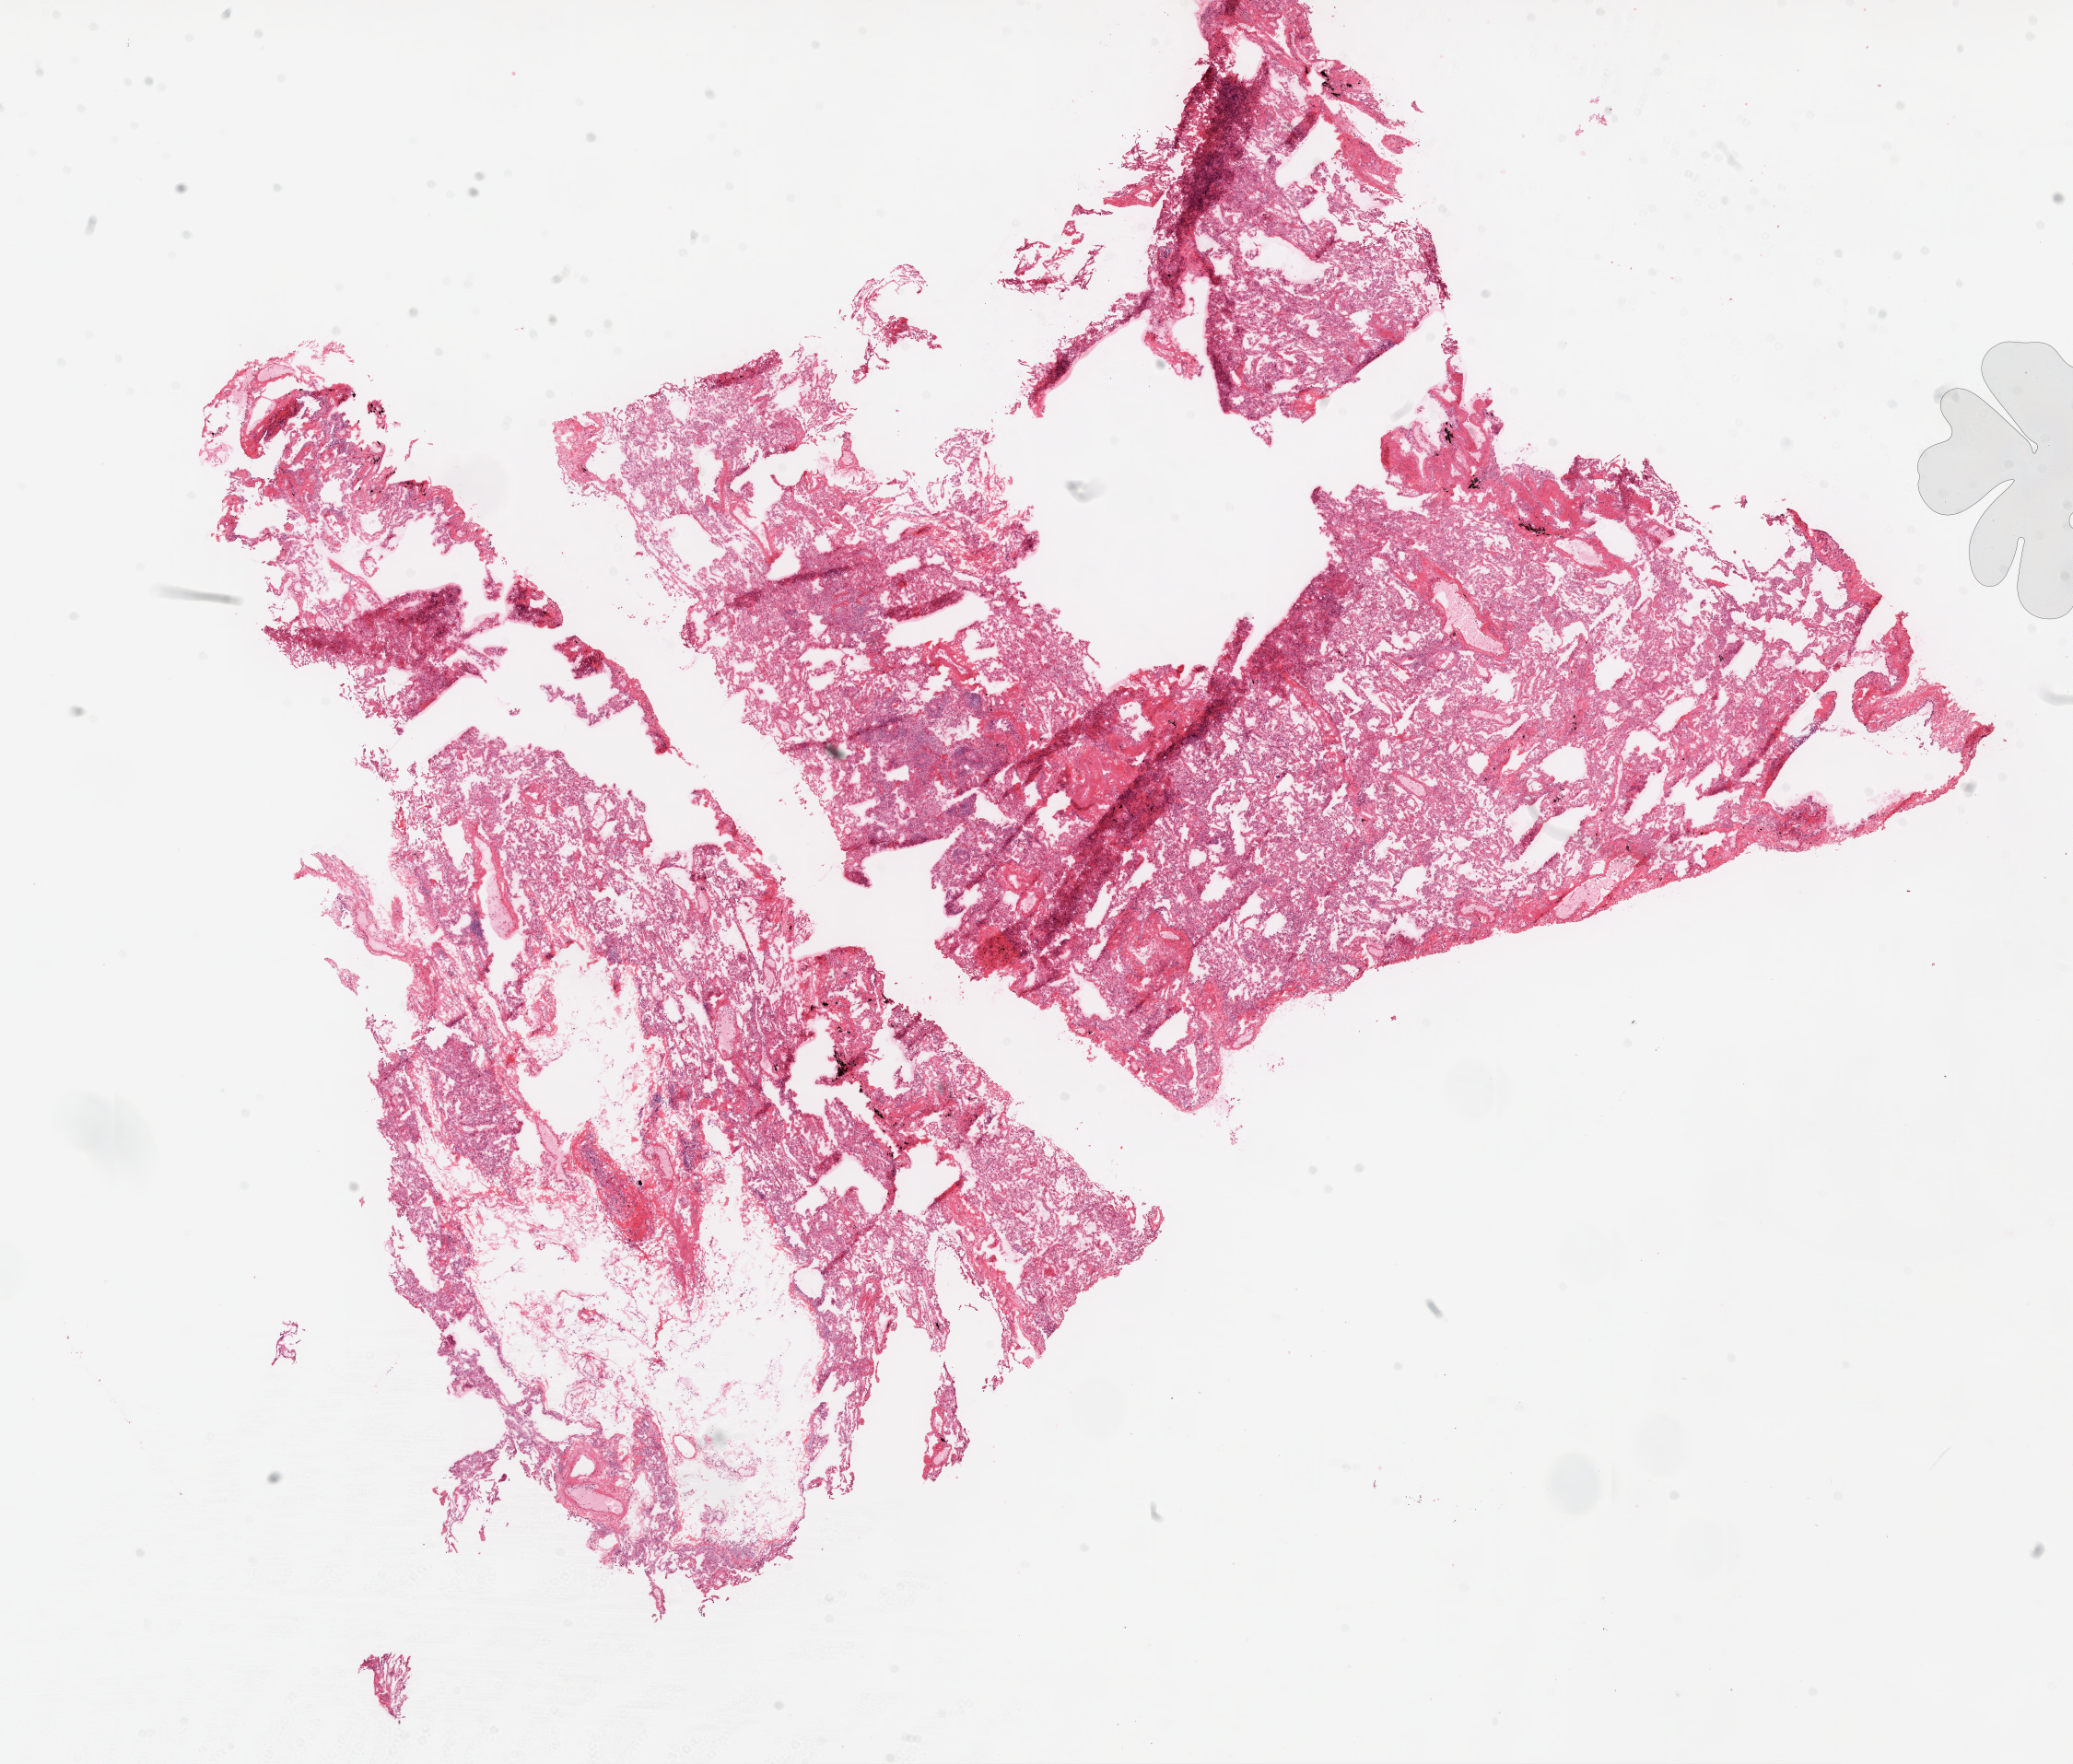
Whole-slide histology image, H&E — shown as a low-resolution overview of the whole scanned area (about 18.1 x 15.4 mm). Frozen section from the top of the tissue portion. Sample: solid tissue normal (non-tumour tissue), lung. Male patient; age at initial diagnosis 70 years.
- this section: solid tissue normal (non-tumour) sample from the same patient
- patient diagnosis: Squamous cell carcinoma, NOS (upper lobe, lung)